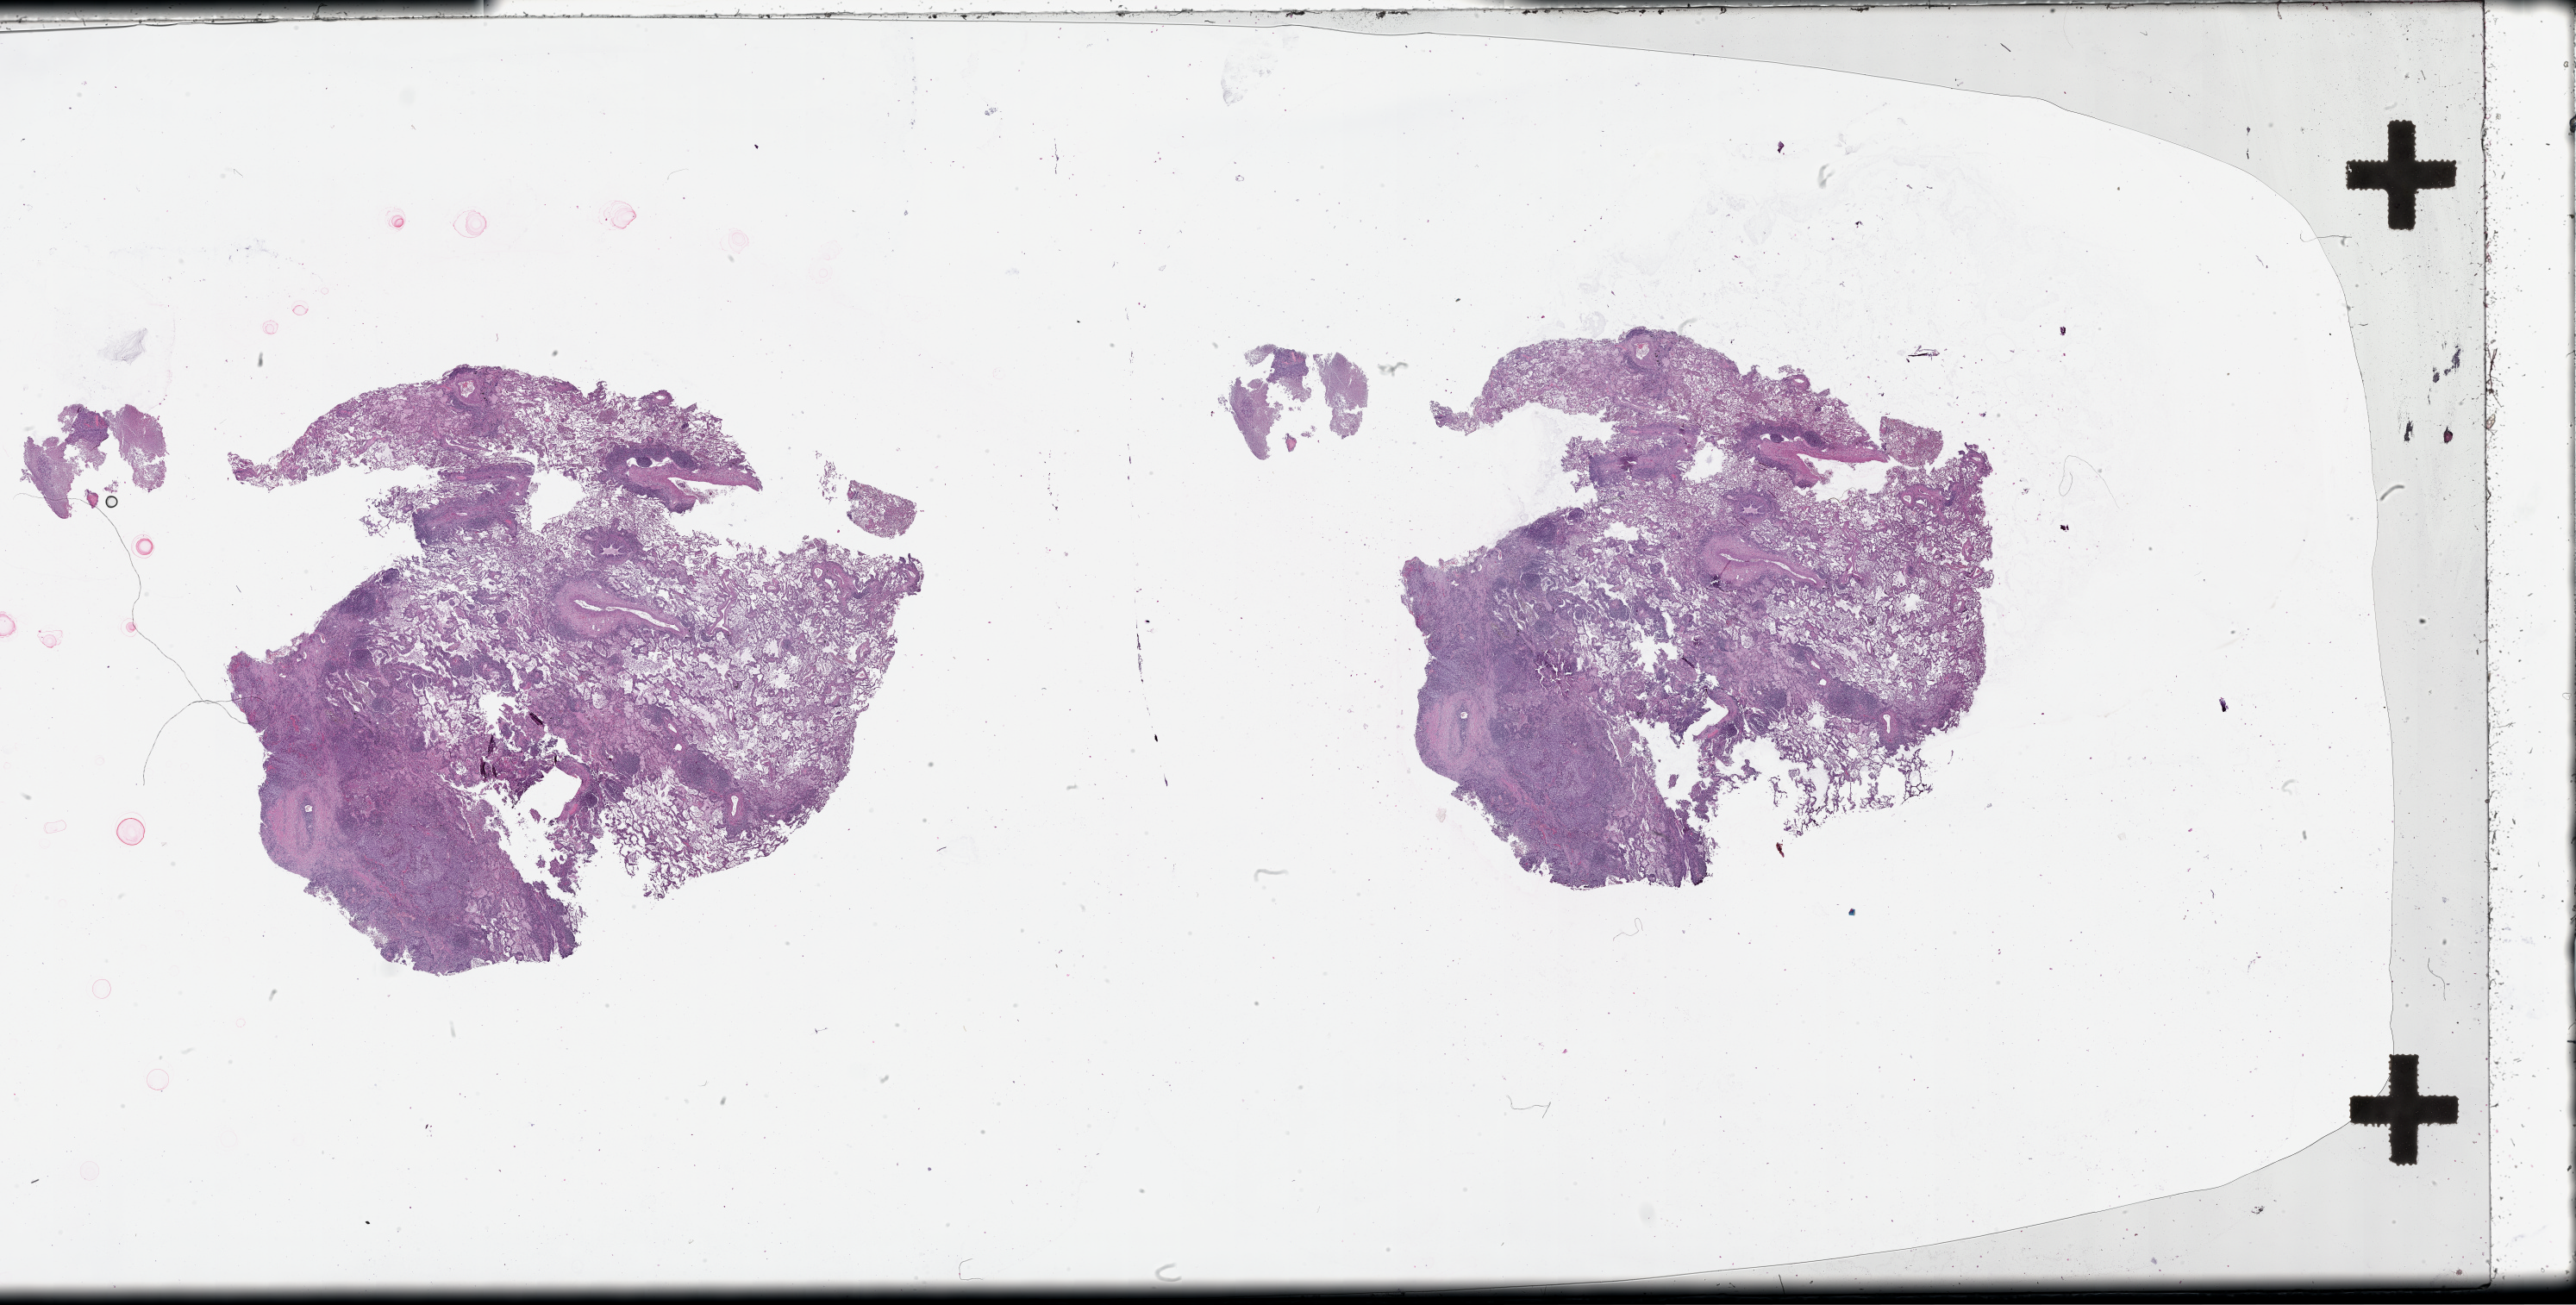
H&E-stained whole-slide image, low-resolution overview of the scanned area, about 48.1 x 24.4 mm (acquisition: 20x scan); tumour tissue sample, lung. Female, 58 y/o.
- patient diagnosis (cohort enrolment): squamous cell carcinoma (lung)